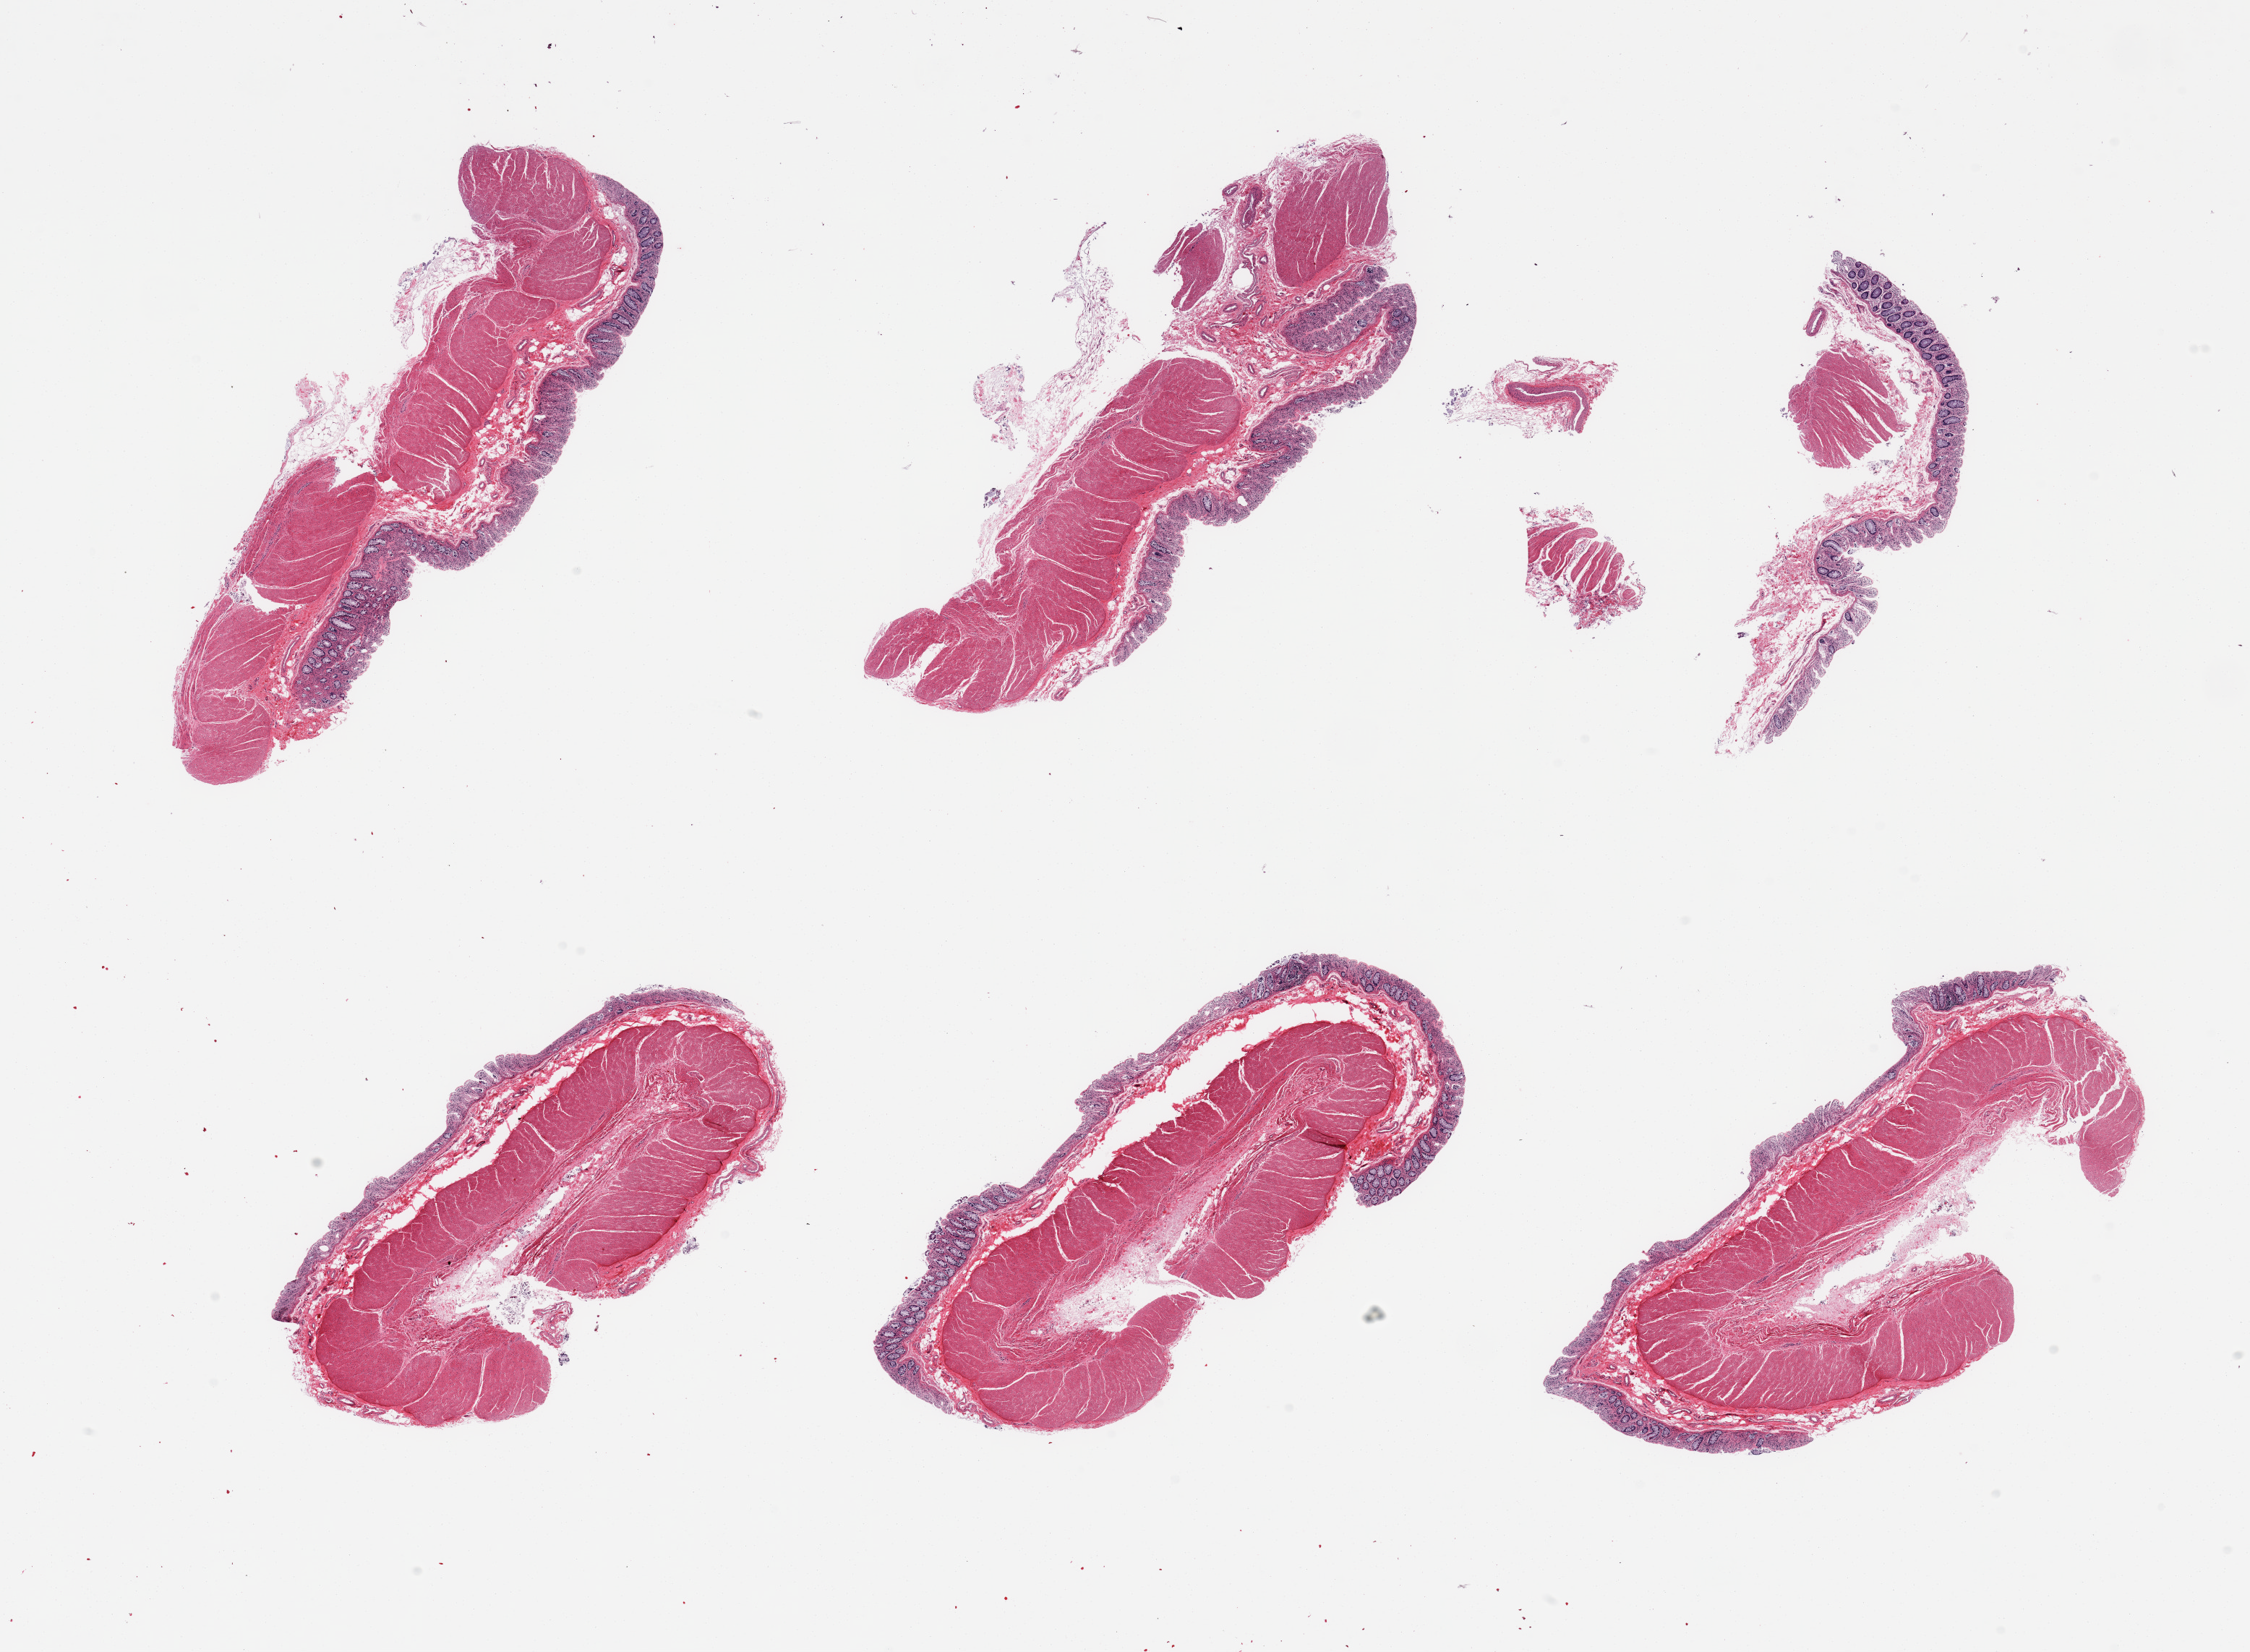
H&E whole-slide image, brightfield, low-resolution overview of the scanned area, about 24.6 x 18.1 mm (acquisition: 20x scan). Donor sex: male.
* specimen: PAXgene-fixed, paraffin-embedded tissue; section of sigmoid colon (target tissue); donor tissue sample